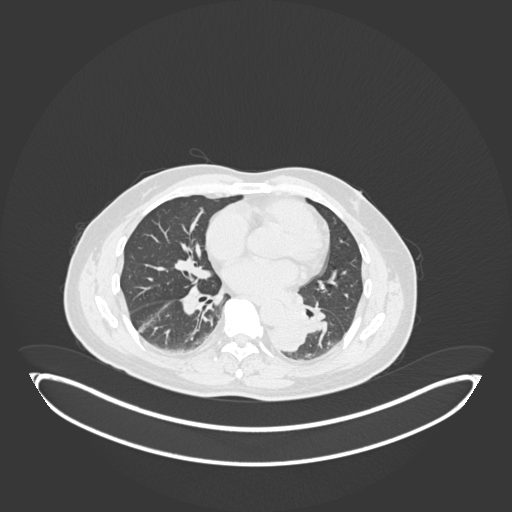
Chest CT, one axial slice; position 85 of 258 along the scan axis; lung window (W 1500 / L -600 HU); 1 mm slice thickness; 512 × 512 image matrix. Male patient, age 54 years. From the clinical record (not read from this slice): clinical TNM (as recorded): T3 N0 M0.
Structures marked on this image (rectangle marked by the reading radiologist):
- lung tumour (recorded histology: squamous cell carcinoma): box from (x=269, y=304) to (x=310, y=356) px